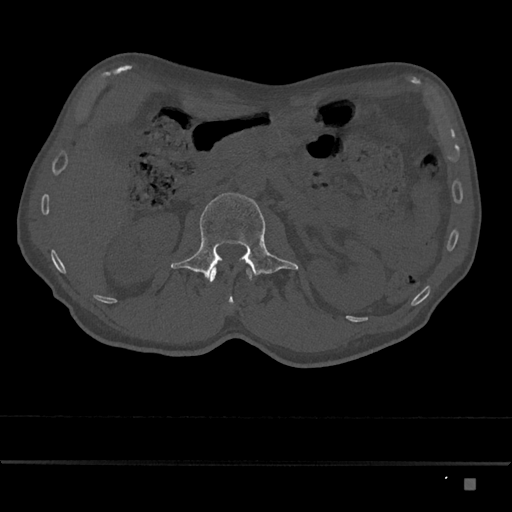
CT including the spine, one axial slice; position 492 of 797 along the scan axis; reconstruction kernel Br40s/3; bone window (W 1800 / L 400 HU); 0.5 mm slice thickness; 512 × 512 image matrix, field of view 390 × 390 mm. Male patient, age 72 years. Case-level facts recorded for this patient, not image findings: primary cancer: prostate.
Structures marked on this image (semi-automatically segmented with operator editing):
- L1 vertebra: bounding box [x1, y1, x2, y2] px = [210, 267, 252, 304]
- L2 vertebra: [171, 193, 298, 281]